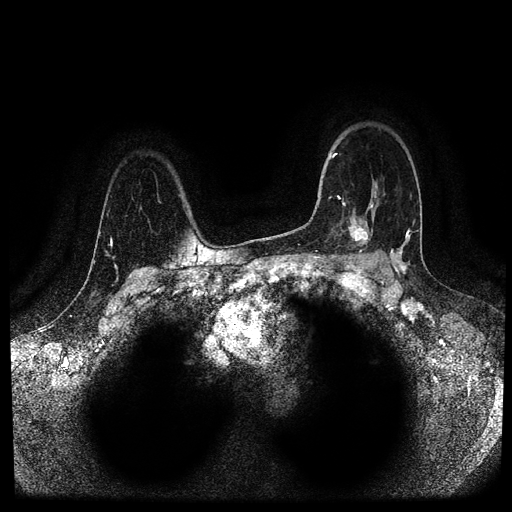
Breast MRI (dynamic contrast-enhanced, multi-phase), one axial slice; position 76 of 116 along the scan axis; dynamic contrast-enhanced series, time point 2 of 5 at this slice position (early post-contrast); 1.5 T; TE 2.6 ms, TR 5.3 ms; 512 × 512 image matrix, field of view 350 × 350 mm. Patient: female, 44 years.
Outlined on this slice (semi-automatically segmented with operator editing):
- breast lesion (labelled 'tumour' in the annotation; benign lesions carry a separate 'benign' label): box from (x=341, y=216) to (x=374, y=251) px